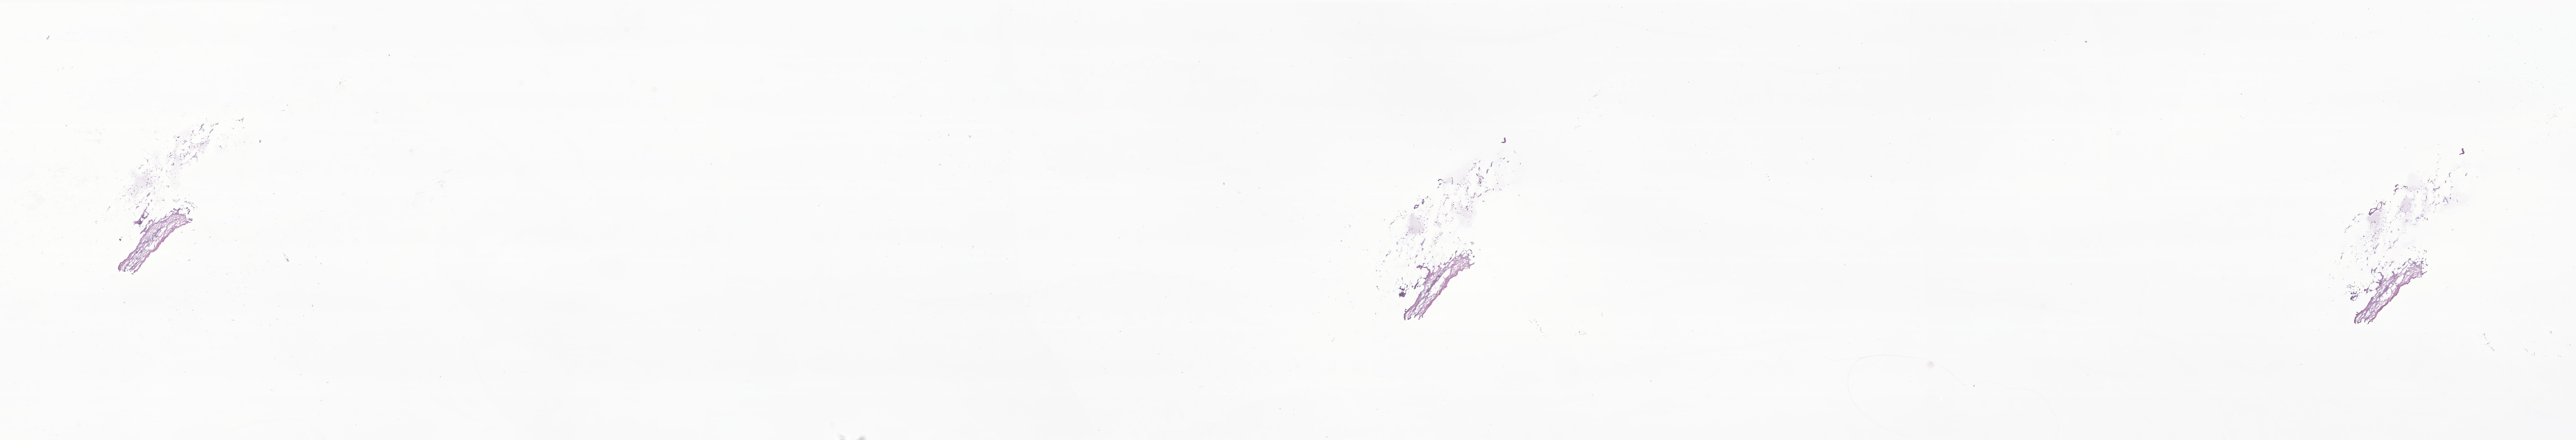
Hematoxylin and eosin (H&E) whole-slide image of tumor tissue from the soft tissue of lower extremity — a low-resolution overview of the entire scanned area, about 41.2 x 7.0 mm, frozen section (OCT-embedded). Patient male; age 212 months (17 years 8 months).
* diagnosis (ICD-O-3 morphology term): Spindle cell sarcoma